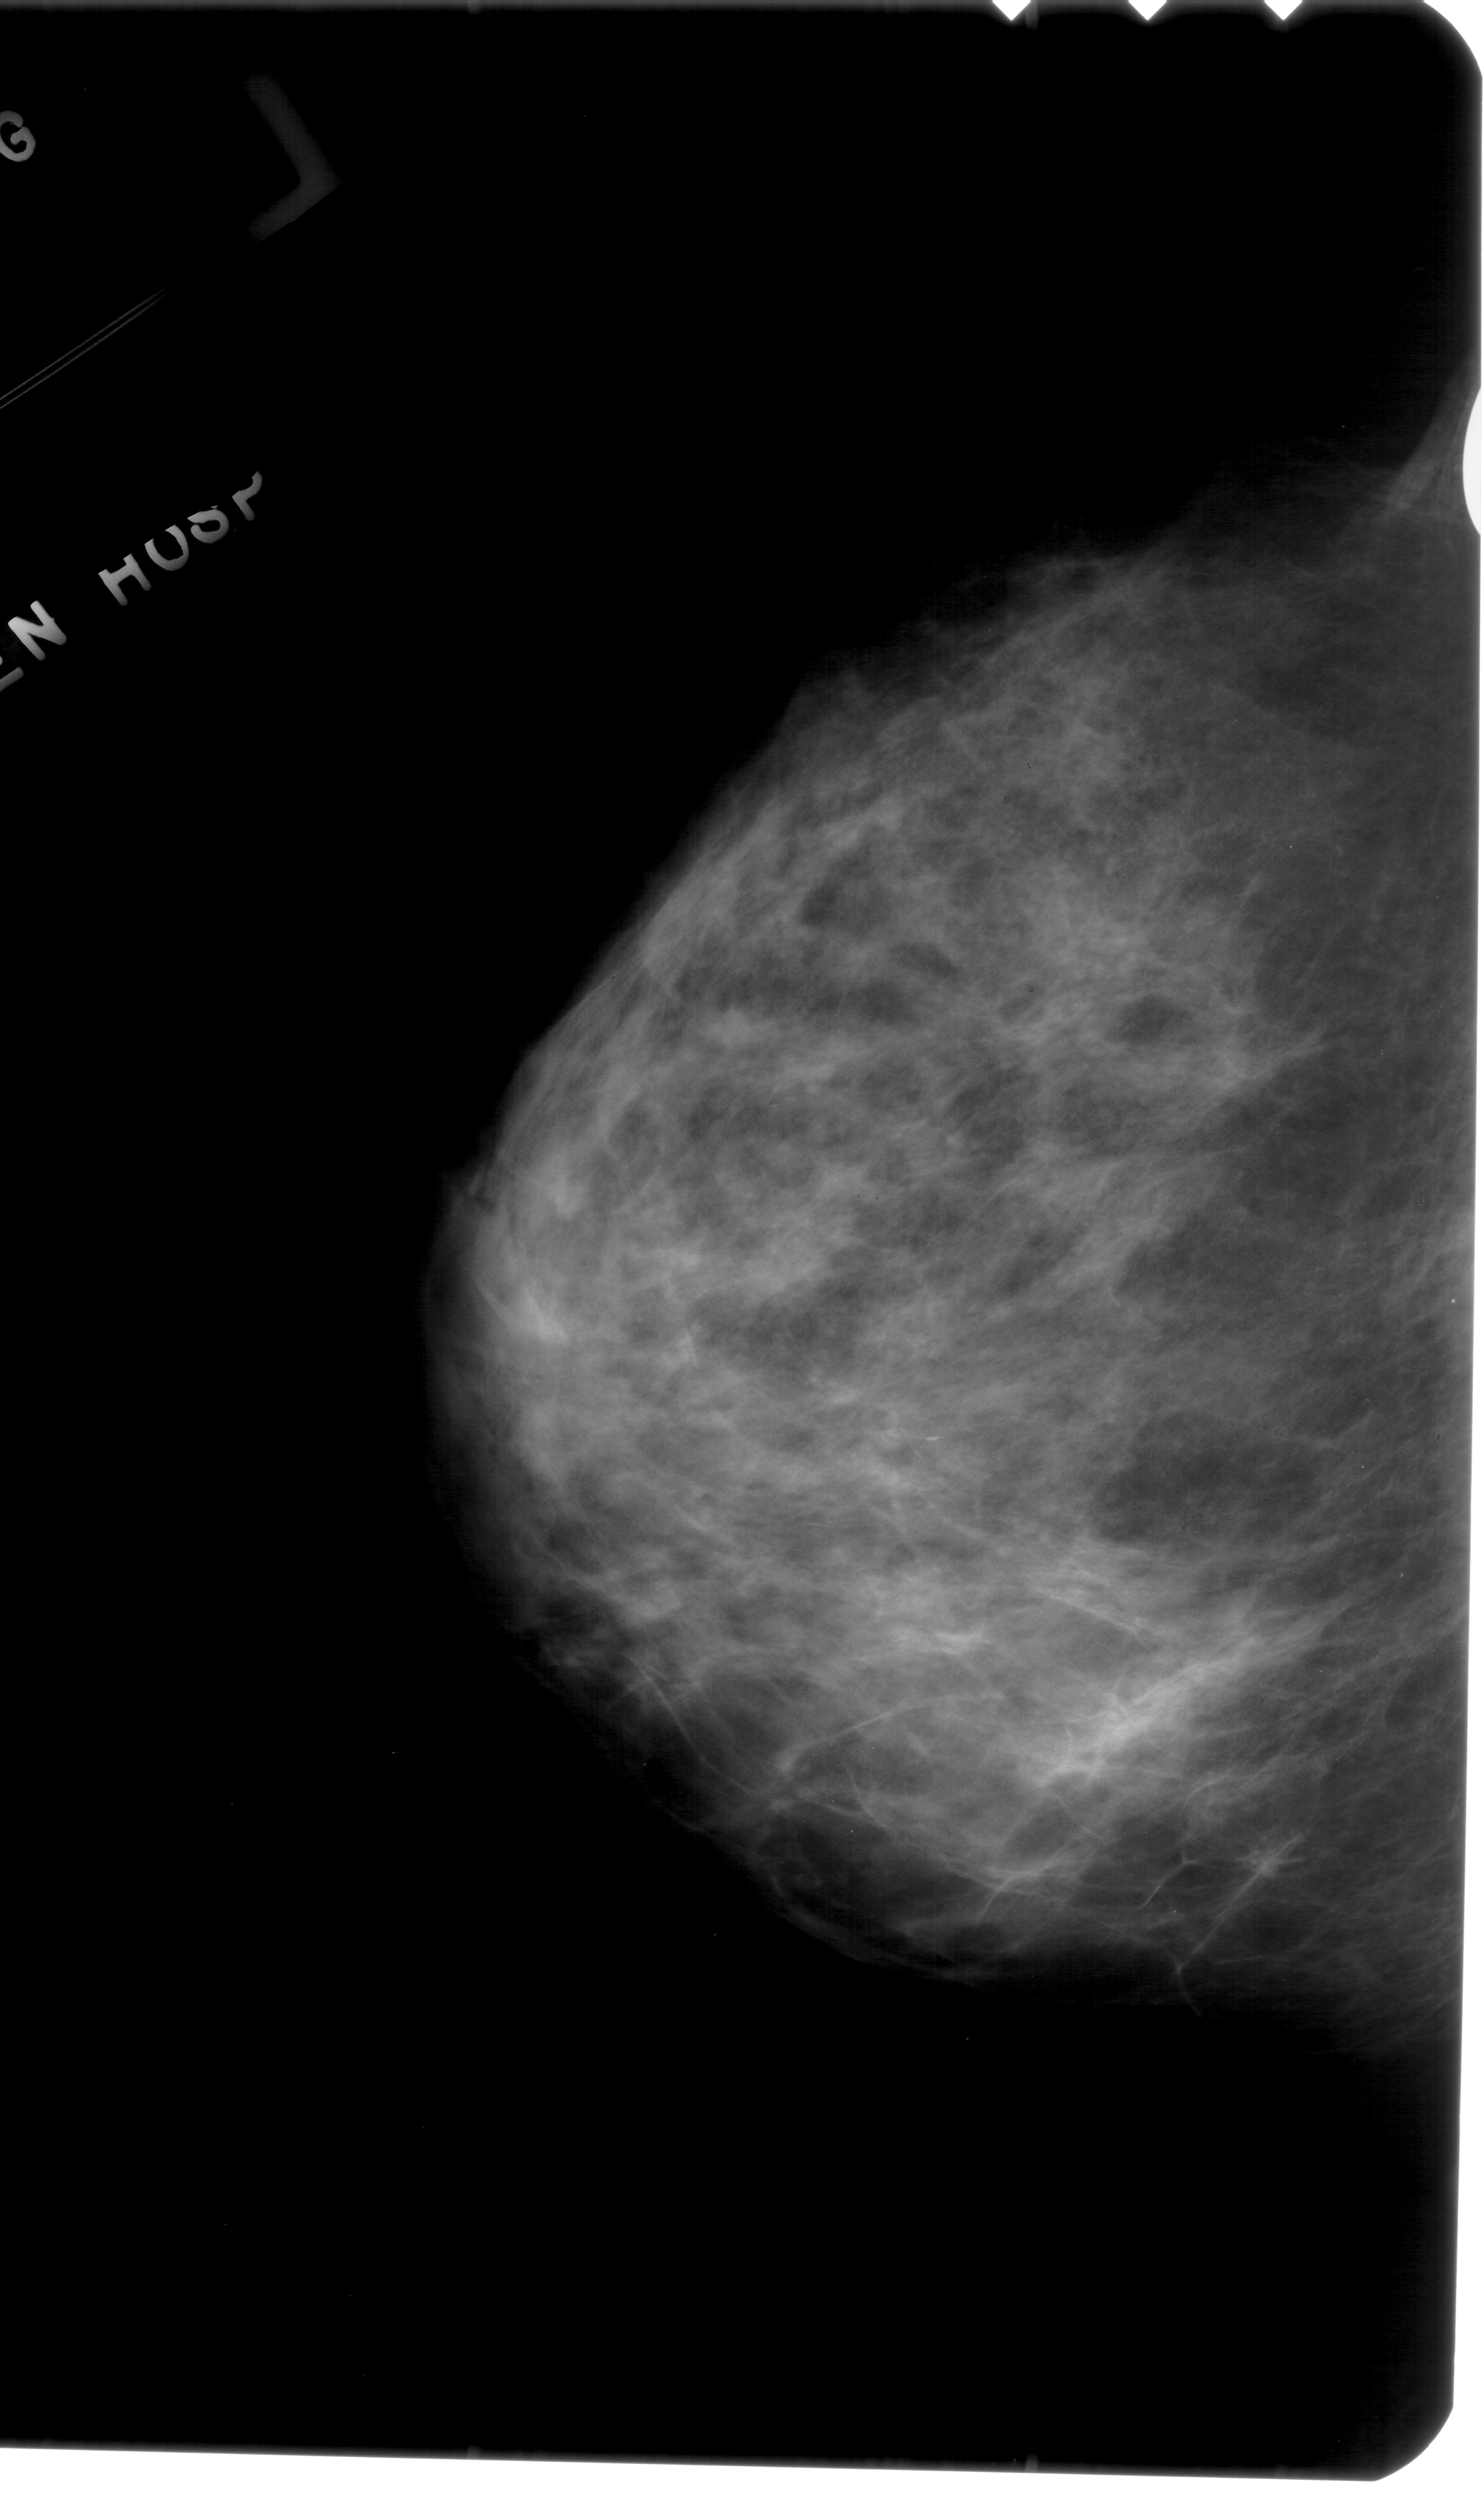
Mammogram (digitized film), left breast, CC view.
Radiologist-marked abnormalities on this image: calcifications, morphology fine linear branching, distribution linear; BI-RADS assessment category 4; pathology (as recorded): malignant.